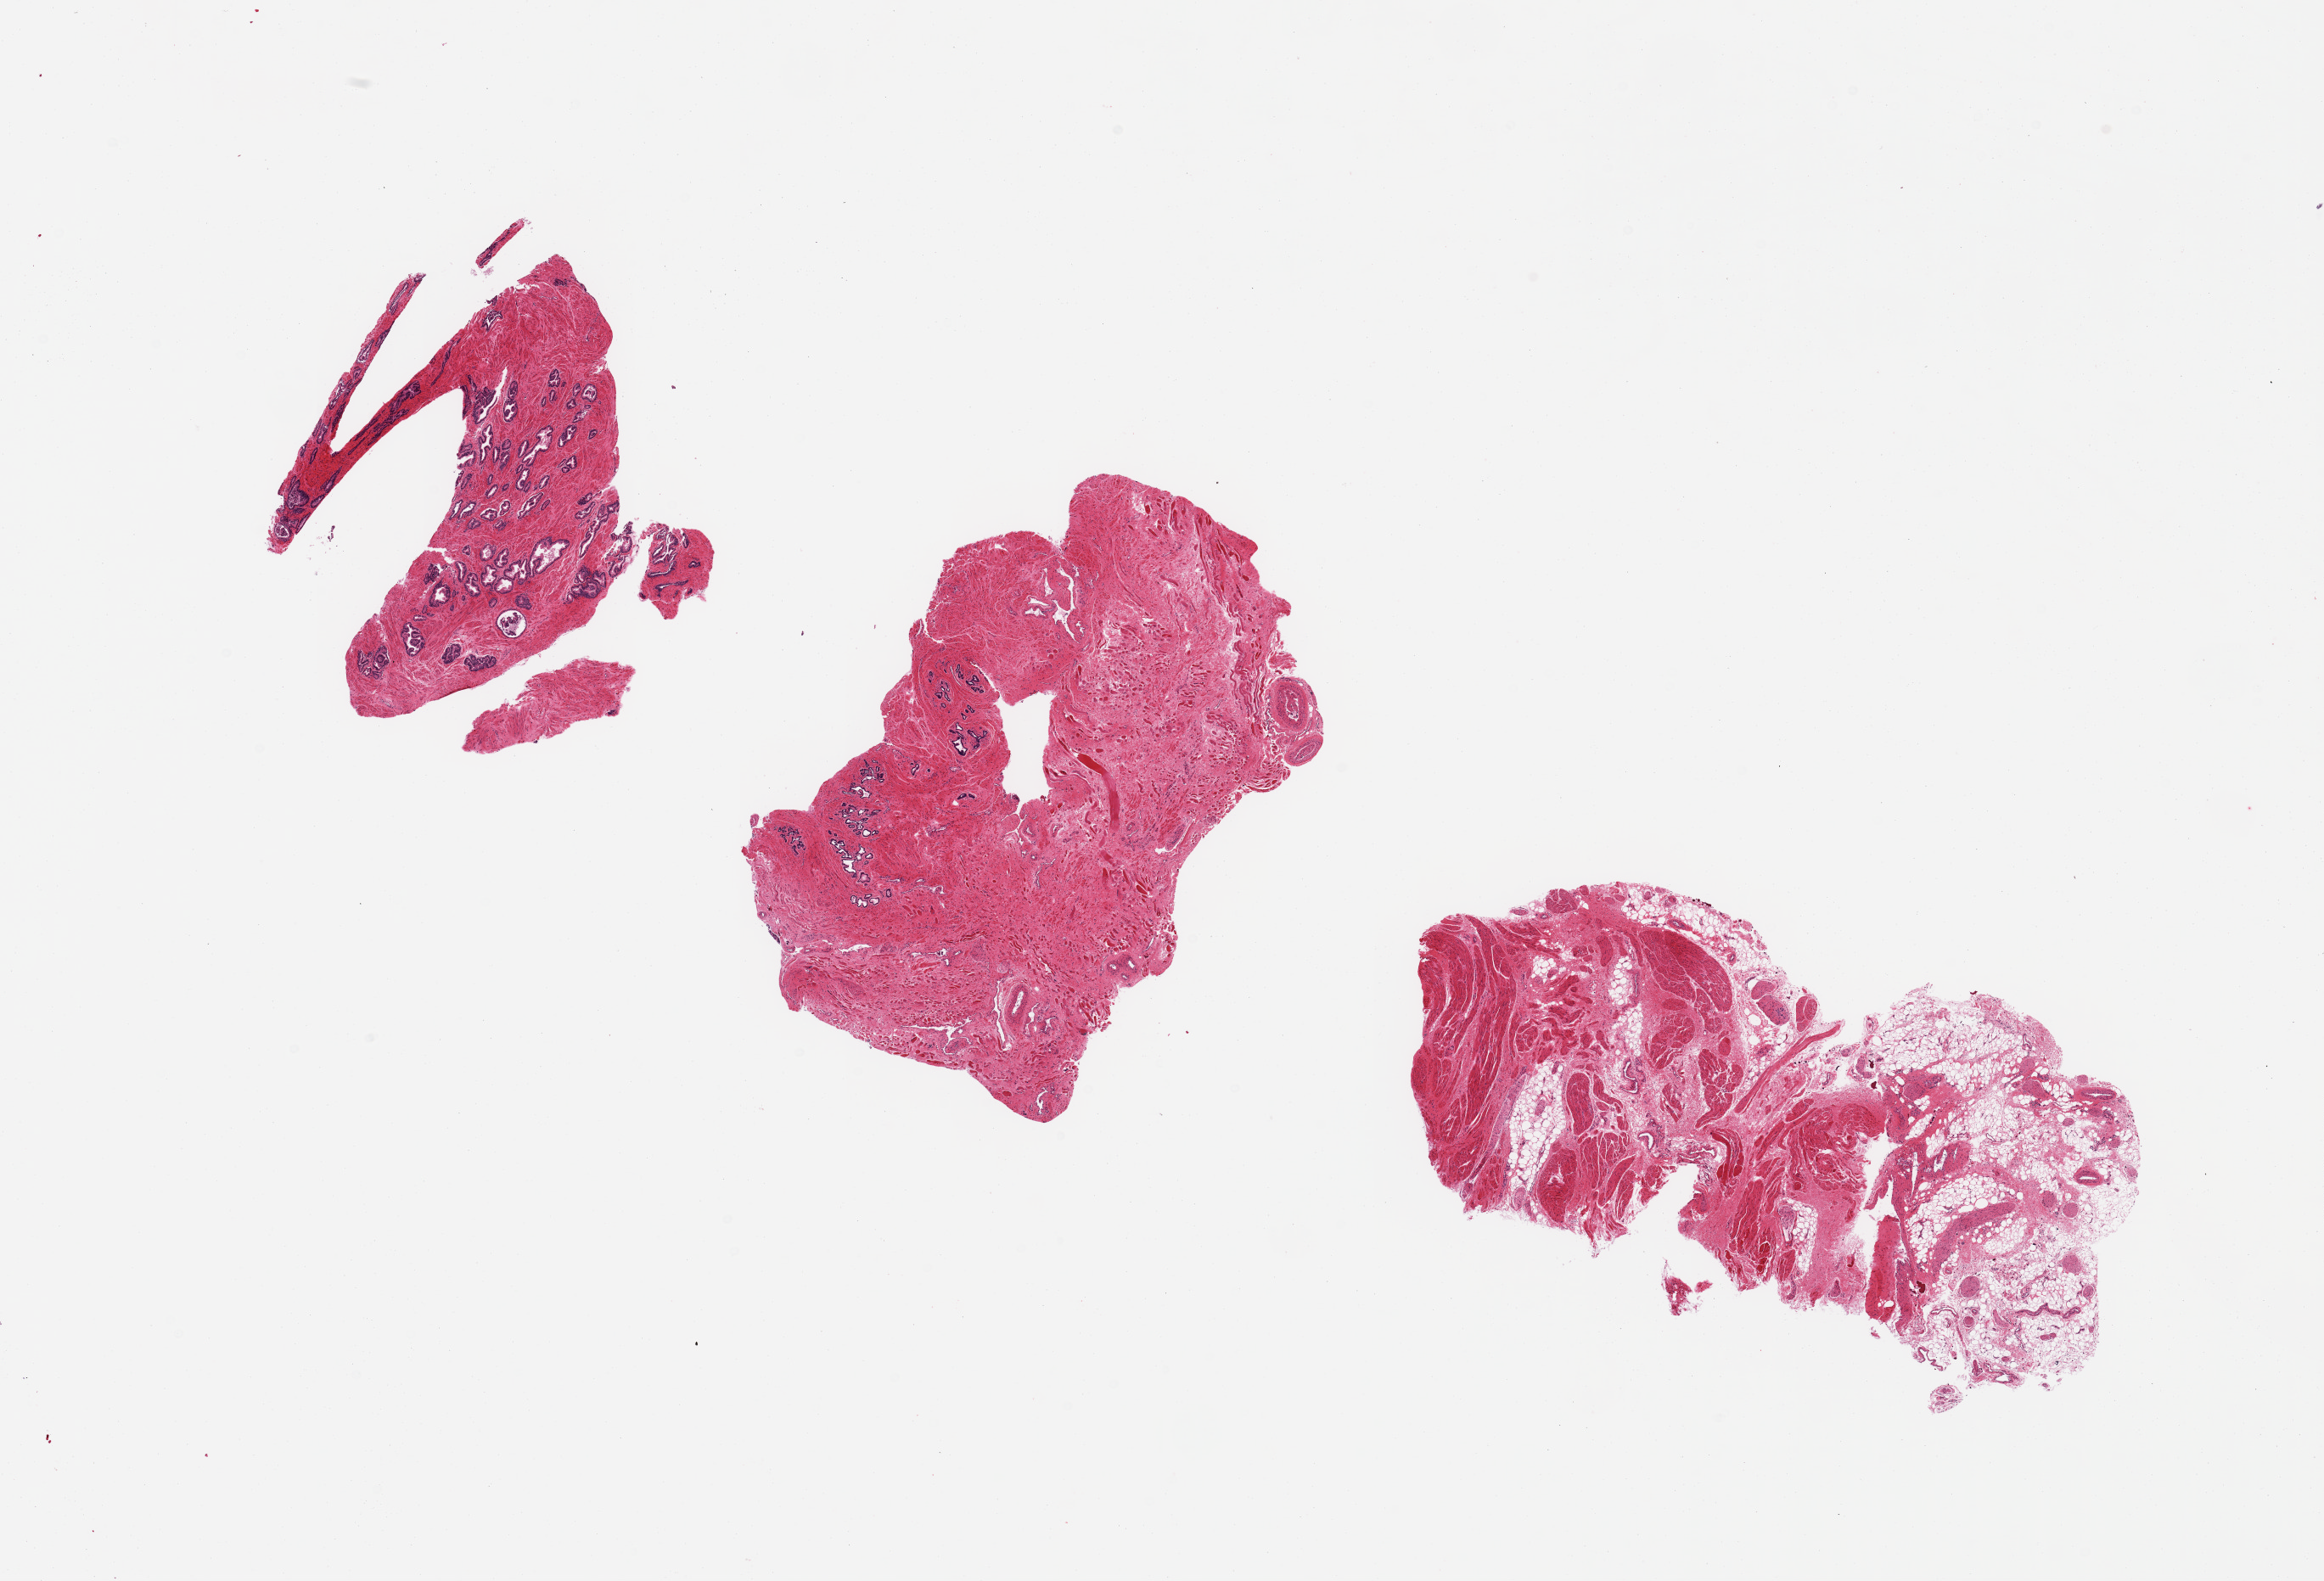
Digitized hematoxylin and eosin (H&E)-stained section — low-resolution overview of the scanned area, about 21.7 x 14.7 mm; PAXgene-fixed, paraffin-embedded tissue; target tissue: prostate; donor tissue sample. Male donor.
Reviewer comment on this tissue sample: 3 pieces; fibromuscular stroma and glandular component; one piece of fibromuscular tissue with vessels fat, and nerves.